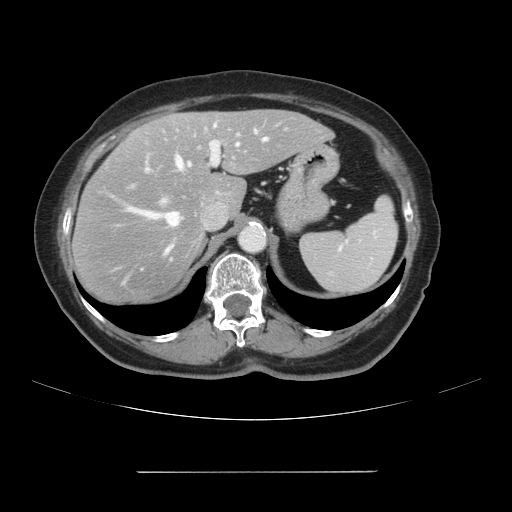
Contrast-enhanced abdominal CT, one axial slice. Position 72 of 111 along the scan axis. 120 kVp. Intravenous contrast given. Soft-tissue window (W 400 / L 40 HU). 2.5 mm slice thickness. 512 × 512 image matrix. Female patient, age 74 years. From the clinical record (not read from this slice): diagnosis: colorectal cancer liver metastases, imaged before liver resection; multiple liver metastases: yes; largest metastasis: 1.1 cm.
Annotated regions visible in this slice (expert manual segmentation):
- hepatic veins: bounding box [x1, y1, x2, y2] px = [114, 130, 268, 285]
- liver: [74, 110, 331, 305]
- planned liver remnant (the part of the liver to remain after resection): [153, 110, 331, 215]
- portal vein (with intrahepatic branches): [146, 125, 219, 203]